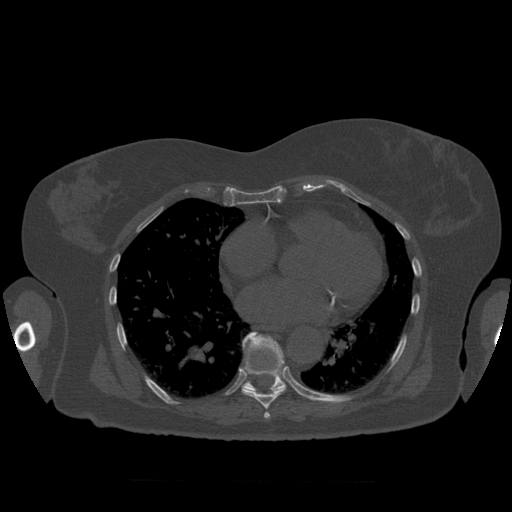
CT including the spine, one axial slice; position 371 of 399 along the scan axis; reconstruction kernel STANDARD; 120 kVp; bone window (W 1800 / L 400 HU); 1.25 mm slice thickness; 512 × 512 image matrix, field of view 404 × 404 mm. Patient age 81 years. Case-level facts recorded for this patient, not image findings: primary cancer: renal.
Annotated regions visible in this slice (semi-automatic segmentation, software-assisted and operator-edited):
- T7 vertebra: box from (x=264, y=412) to (x=271, y=419) px
- T8 vertebra: (x=242, y=343)–(x=286, y=410)
- T9 vertebra: (x=243, y=332)–(x=300, y=395)